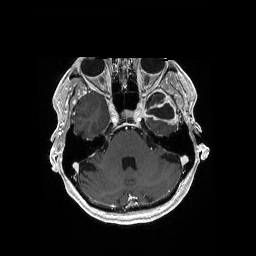
Brain MRI from a brain-tumour surgery series, one axial slice. Slice 129 of 176 in the series (ordered by position). T1-weighted post-contrast. 1 mm slice thickness. 256 × 256 image matrix, field of view 256 × 256 mm. Case-level facts recorded for this patient, not image findings: histopathology: Glioblastoma; WHO grade: 4; IDH mutation: no.
Outlined on this slice (expert manual segmentation):
- previous resection cavity: bounding box [x1, y1, x2, y2] px = [149, 103, 174, 119]
- tumour: [151, 116, 178, 125]